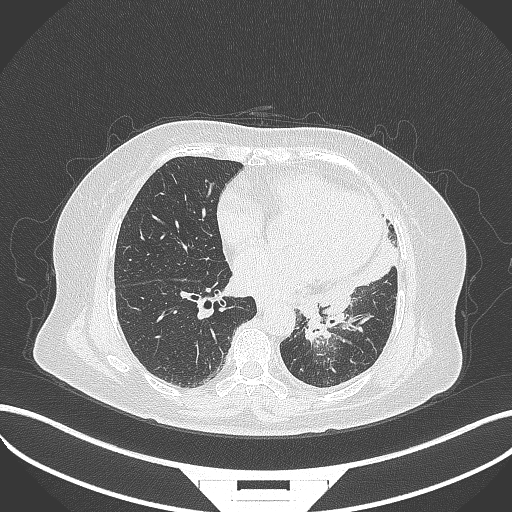
Chest CT, one axial slice. Lung window (W 1500 / L -600 HU). 512 × 512 image matrix, field of view 400 × 400 mm. Female patient, age 69 years. Case-level facts recorded for this patient, not image findings: clinical TNM (as recorded): T2b N3 M1.
Annotated regions visible in this slice (rectangle marked by the reading radiologist):
- lung tumour (recorded histology: adenocarcinoma): box from (x=298, y=314) to (x=335, y=346) px